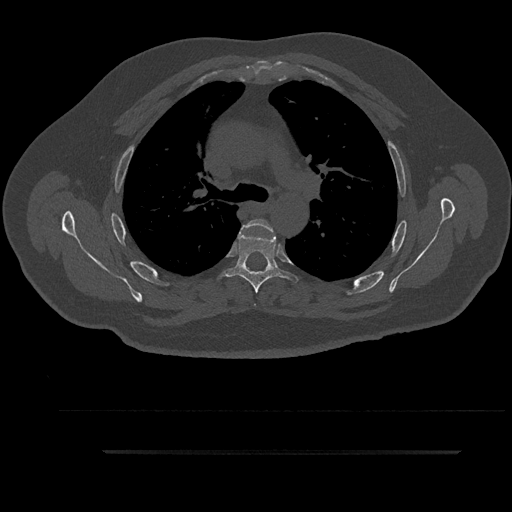
CT including the spine, one axial slice. Slice 634 of 797 in the series (ordered by position). 120 kVp. Bone window (W 1800 / L 400 HU). 0.5 mm slice thickness. 512 × 512 image matrix. Male patient, age 63 years. From the clinical record (not read from this slice): primary cancer: renal.
Structures marked on this image (semi-automatically segmented with operator editing):
- T4 vertebra: bounding box <239,219,273,235> (left, top, right, bottom; pixels)
- T5 vertebra: <218,229,298,294>
- T6 vertebra: <263,269,266,272>